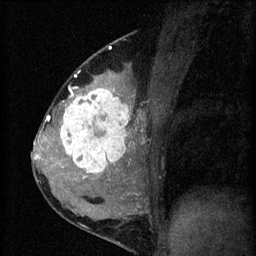
Breast MRI (dynamic contrast-enhanced), one sagittal slice. Slice 31 of 60 in the series (ordered by position). 3 images stored at this slice position (order not interpretable as contrast timing). 1.5 T. TE 4.2 ms, TR 8.2 ms. 2 mm slice thickness. 256 × 256 image matrix, field of view 180 × 180 mm. Patient: female, 37 years.
Outlined on this slice (semi-automatic segmentation, software-assisted and operator-edited):
- analysis volume of interest (the breast-tissue region the enhancement analysis was run in; not a lesion): bounding box (x1, y1, x2, y2) in pixels: (53, 78, 140, 181)
- tumour enhancement mask (voxels above the 70 % enhancement threshold inside the analysis volume of interest): (60, 78, 134, 179)